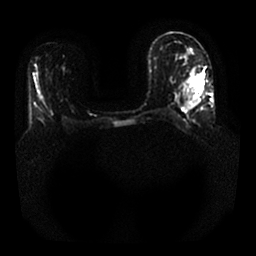
Breast MRI, one axial slice. Slice 11 of 25 in the series (ordered by position). Diffusion-weighted series; image 2 of 4 stored at this slice position (different b-values; order by instance number). 1.5 T. 4 mm slice thickness. 256 × 256 image matrix, field of view 340 × 340 mm. Female patient.
Annotated regions visible in this slice (outlined manually by an expert reader):
- tumour on diffusion-weighted imaging: bounding box [x1, y1, x2, y2] px = [197, 72, 204, 91]